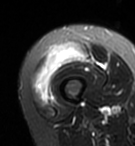
MRI of an extremity soft-tissue mass, one axial slice. Position 14 of 95 along the scan axis. T2-weighted fat-saturated. MR volume resampled by the dataset authors to the PET/CT grid (not the native acquisition matrix). 135 × 146 image matrix, field of view 132 × 143 mm. Female patient. From the clinical record (not read from this slice): histological type: pleiomorphic undifferentiated sarcoma; grade: high; site of the primary tumour: right quadricep.
Outlined on this slice (expert contour drawn on MRI and transferred to this co-registered scan by the dataset authors):
- gross tumour volume including surrounding oedema: box from (x=32, y=43) to (x=88, y=105) px